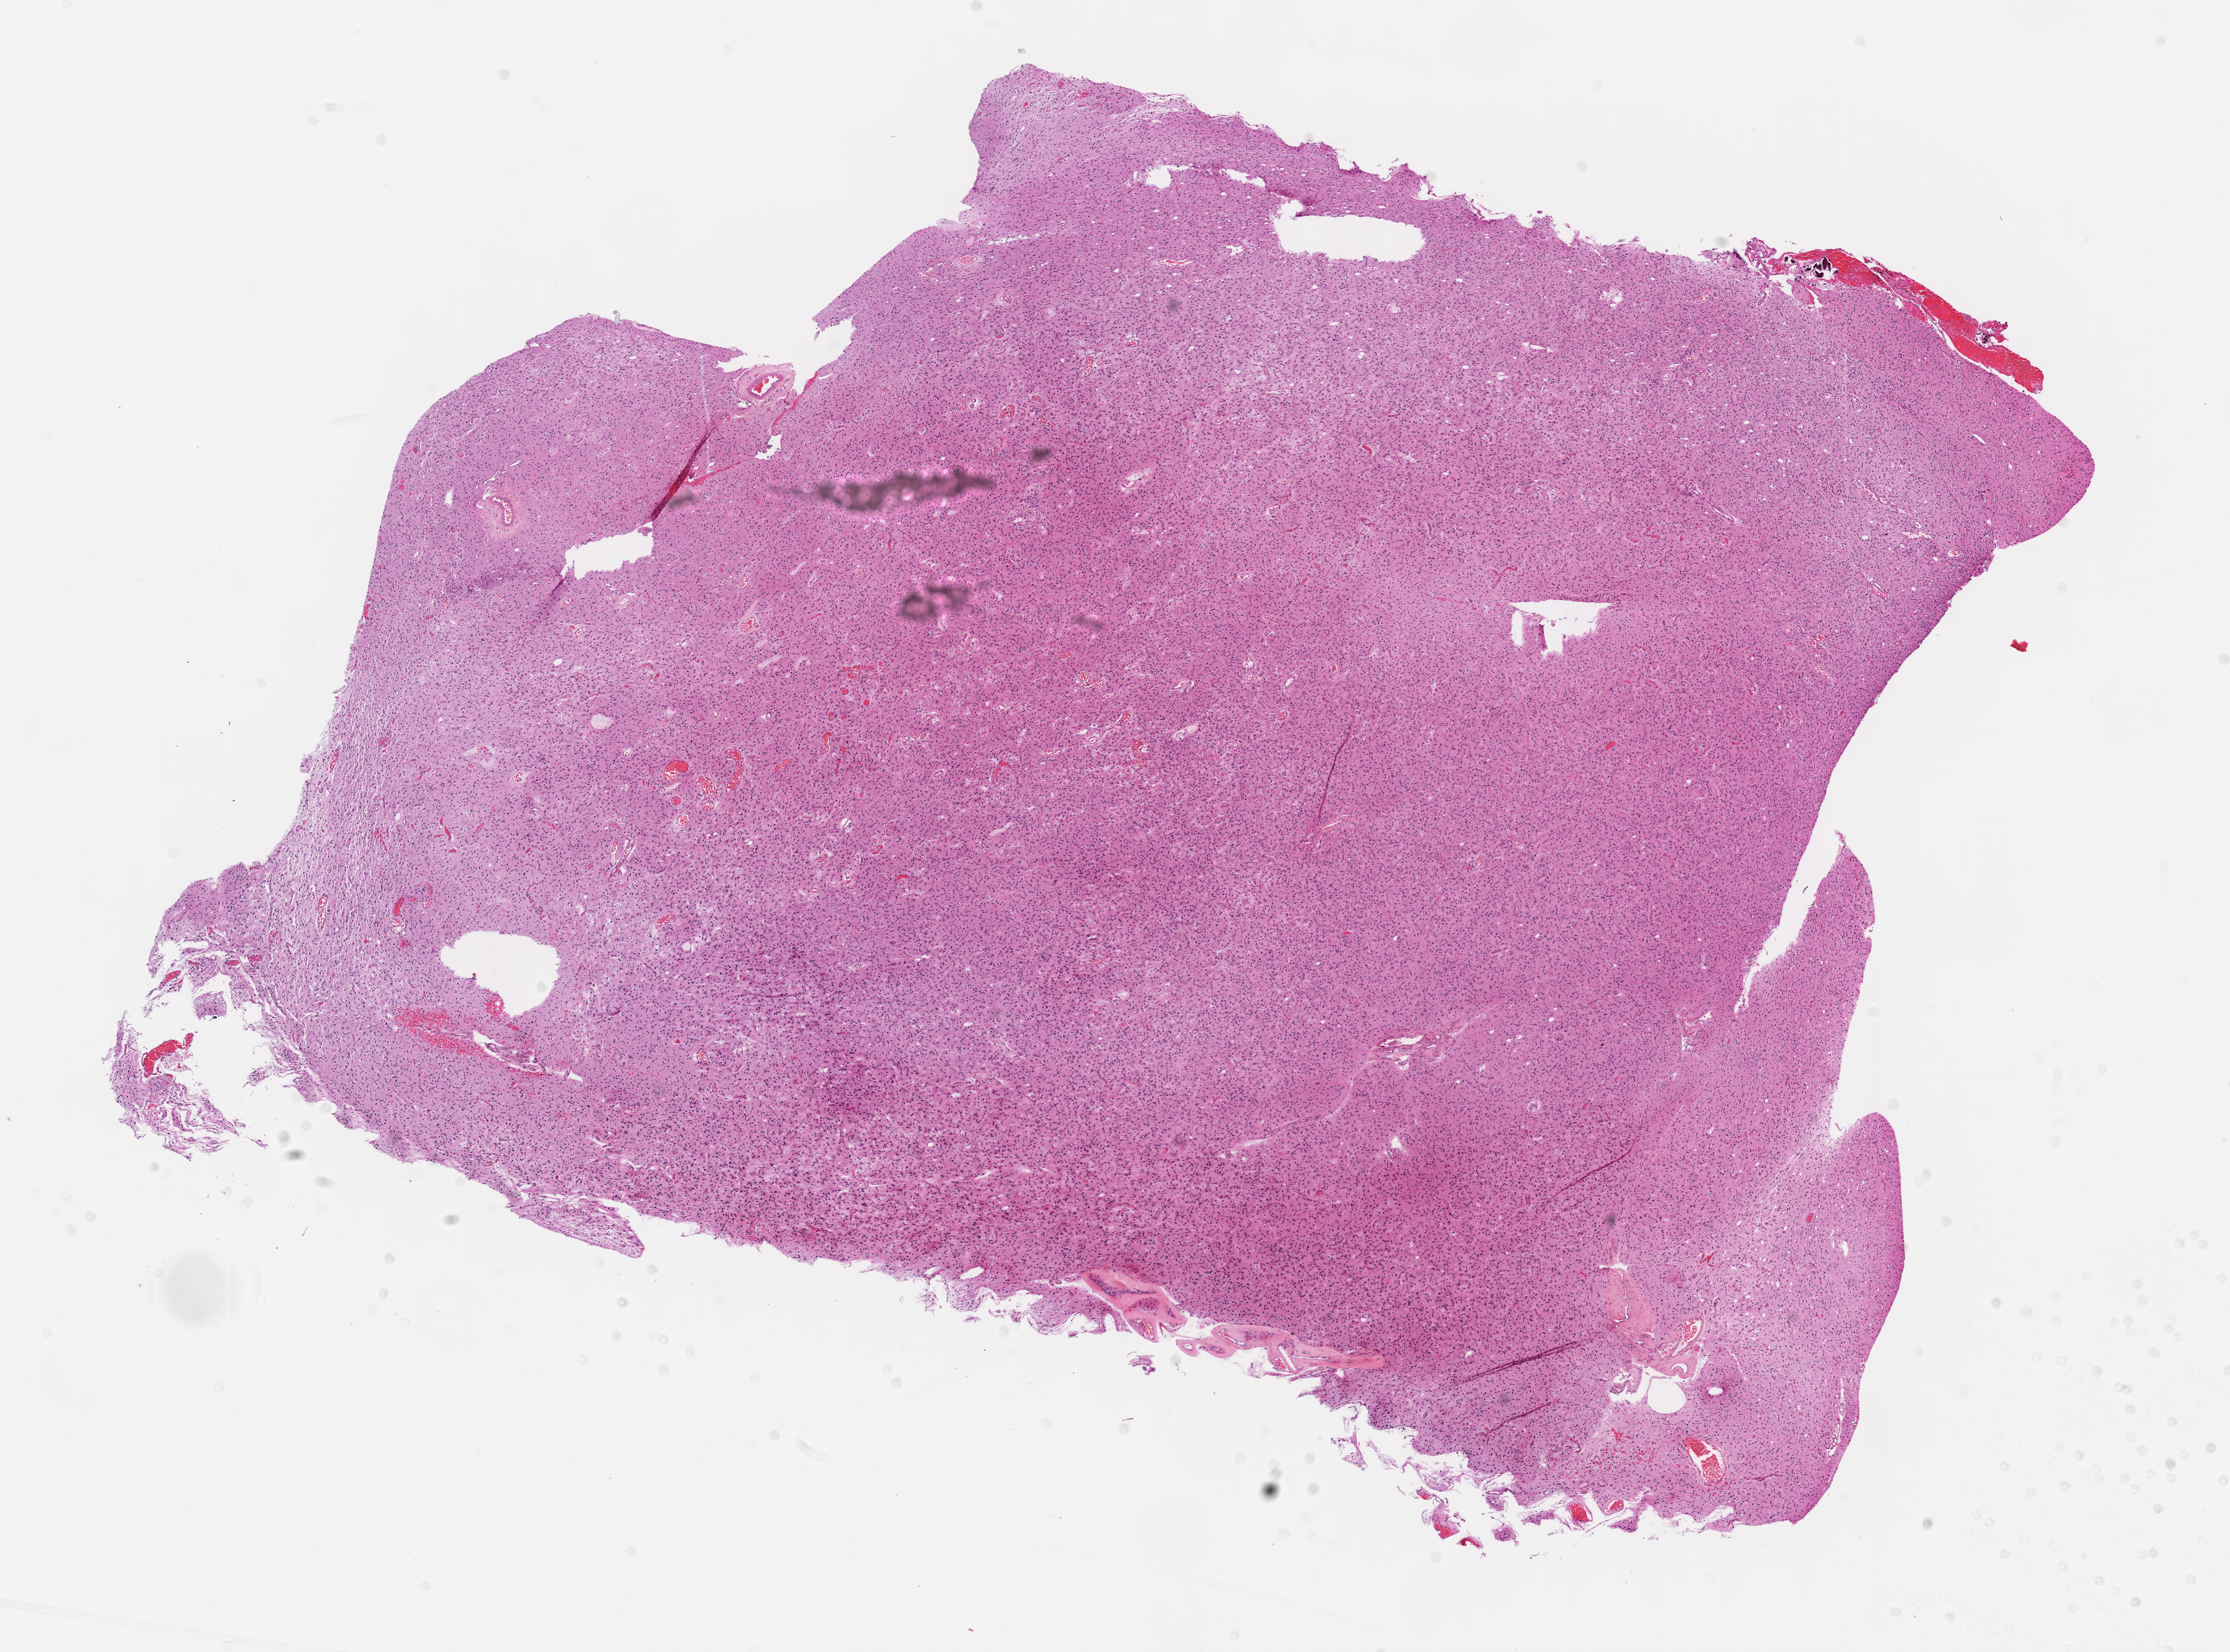
Digitized H&E-stained tissue section (whole slide) — whole scanned area (about 14.6 x 10.8 mm, slide scanned at 40x) shown as a low-resolution overview, FFPE section, sample: primary tumour, brain. Male, age 65 years at initial diagnosis. Histologic grade: G2 (moderately differentiated).
• laterality: right
• pathologic diagnosis: Astrocytoma, NOS (cerebrum)